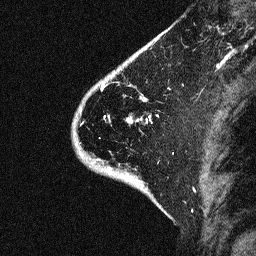
Breast MRI (dynamic contrast-enhanced), one sagittal slice. Position 14 of 64 along the scan axis. Dynamic contrast-enhanced study with each time point stored as its own series, time point 2 of 3 at this slice position (early post-contrast, ordered by acquisition time). 1.5 T. TE 4.5 ms, TR 11 ms. 2.06 mm slice thickness. 256 × 256 image matrix, field of view 200 × 200 mm. Female patient, age 46 years. Case-level facts recorded for this patient, not image findings: setting: breast cancer imaged before/during neoadjuvant chemotherapy; receptor status: HER2-positive.
Structures marked on this image (semi-automatic segmentation, software-assisted and operator-edited):
- analysis volume of interest (the breast-tissue region the enhancement analysis was run in; not a lesion): box from (x=43, y=72) to (x=176, y=177) px
- tumour enhancement mask (voxels above the 90 % enhancement threshold inside the analysis volume of interest): (x=103, y=83)–(x=138, y=123)